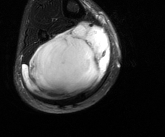
MRI of an extremity soft-tissue mass, one axial slice. Slice 62 of 81 in the series (ordered by position). T2-weighted fat-saturated. MR volume resampled by the dataset authors to the PET/CT grid (not the native acquisition matrix). 165 × 137 image matrix, field of view 161 × 134 mm. Male patient. Case-level facts recorded for this patient, not image findings: histological type: liposarcoma - round cell; grade: high; site of the primary tumour: right calf.
Structures marked on this image (expert contour drawn on MRI and transferred to this co-registered scan by the dataset authors):
- gross tumour volume (mass): bounding box <21,22,111,101> (left, top, right, bottom; pixels)